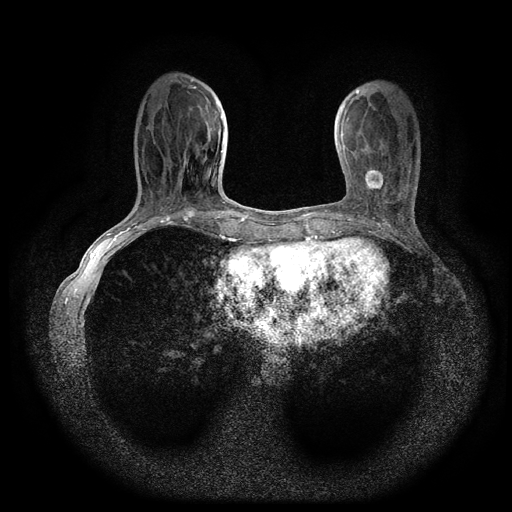
Breast MRI (dynamic contrast-enhanced, multi-phase), one axial slice. Dynamic contrast-enhanced series, time point 2 of 5 at this slice position (early post-contrast). 1.5 T. TE 2.7 ms, TR 5.4 ms. 512 × 512 image matrix, field of view 330 × 330 mm. Patient: female, 49 years.
Structures marked on this image (semi-automatic segmentation, software-assisted and operator-edited):
- breast lesion (labelled 'tumour' in the annotation; benign lesions carry a separate 'benign' label): bounding box <363,164,387,191> (left, top, right, bottom; pixels)